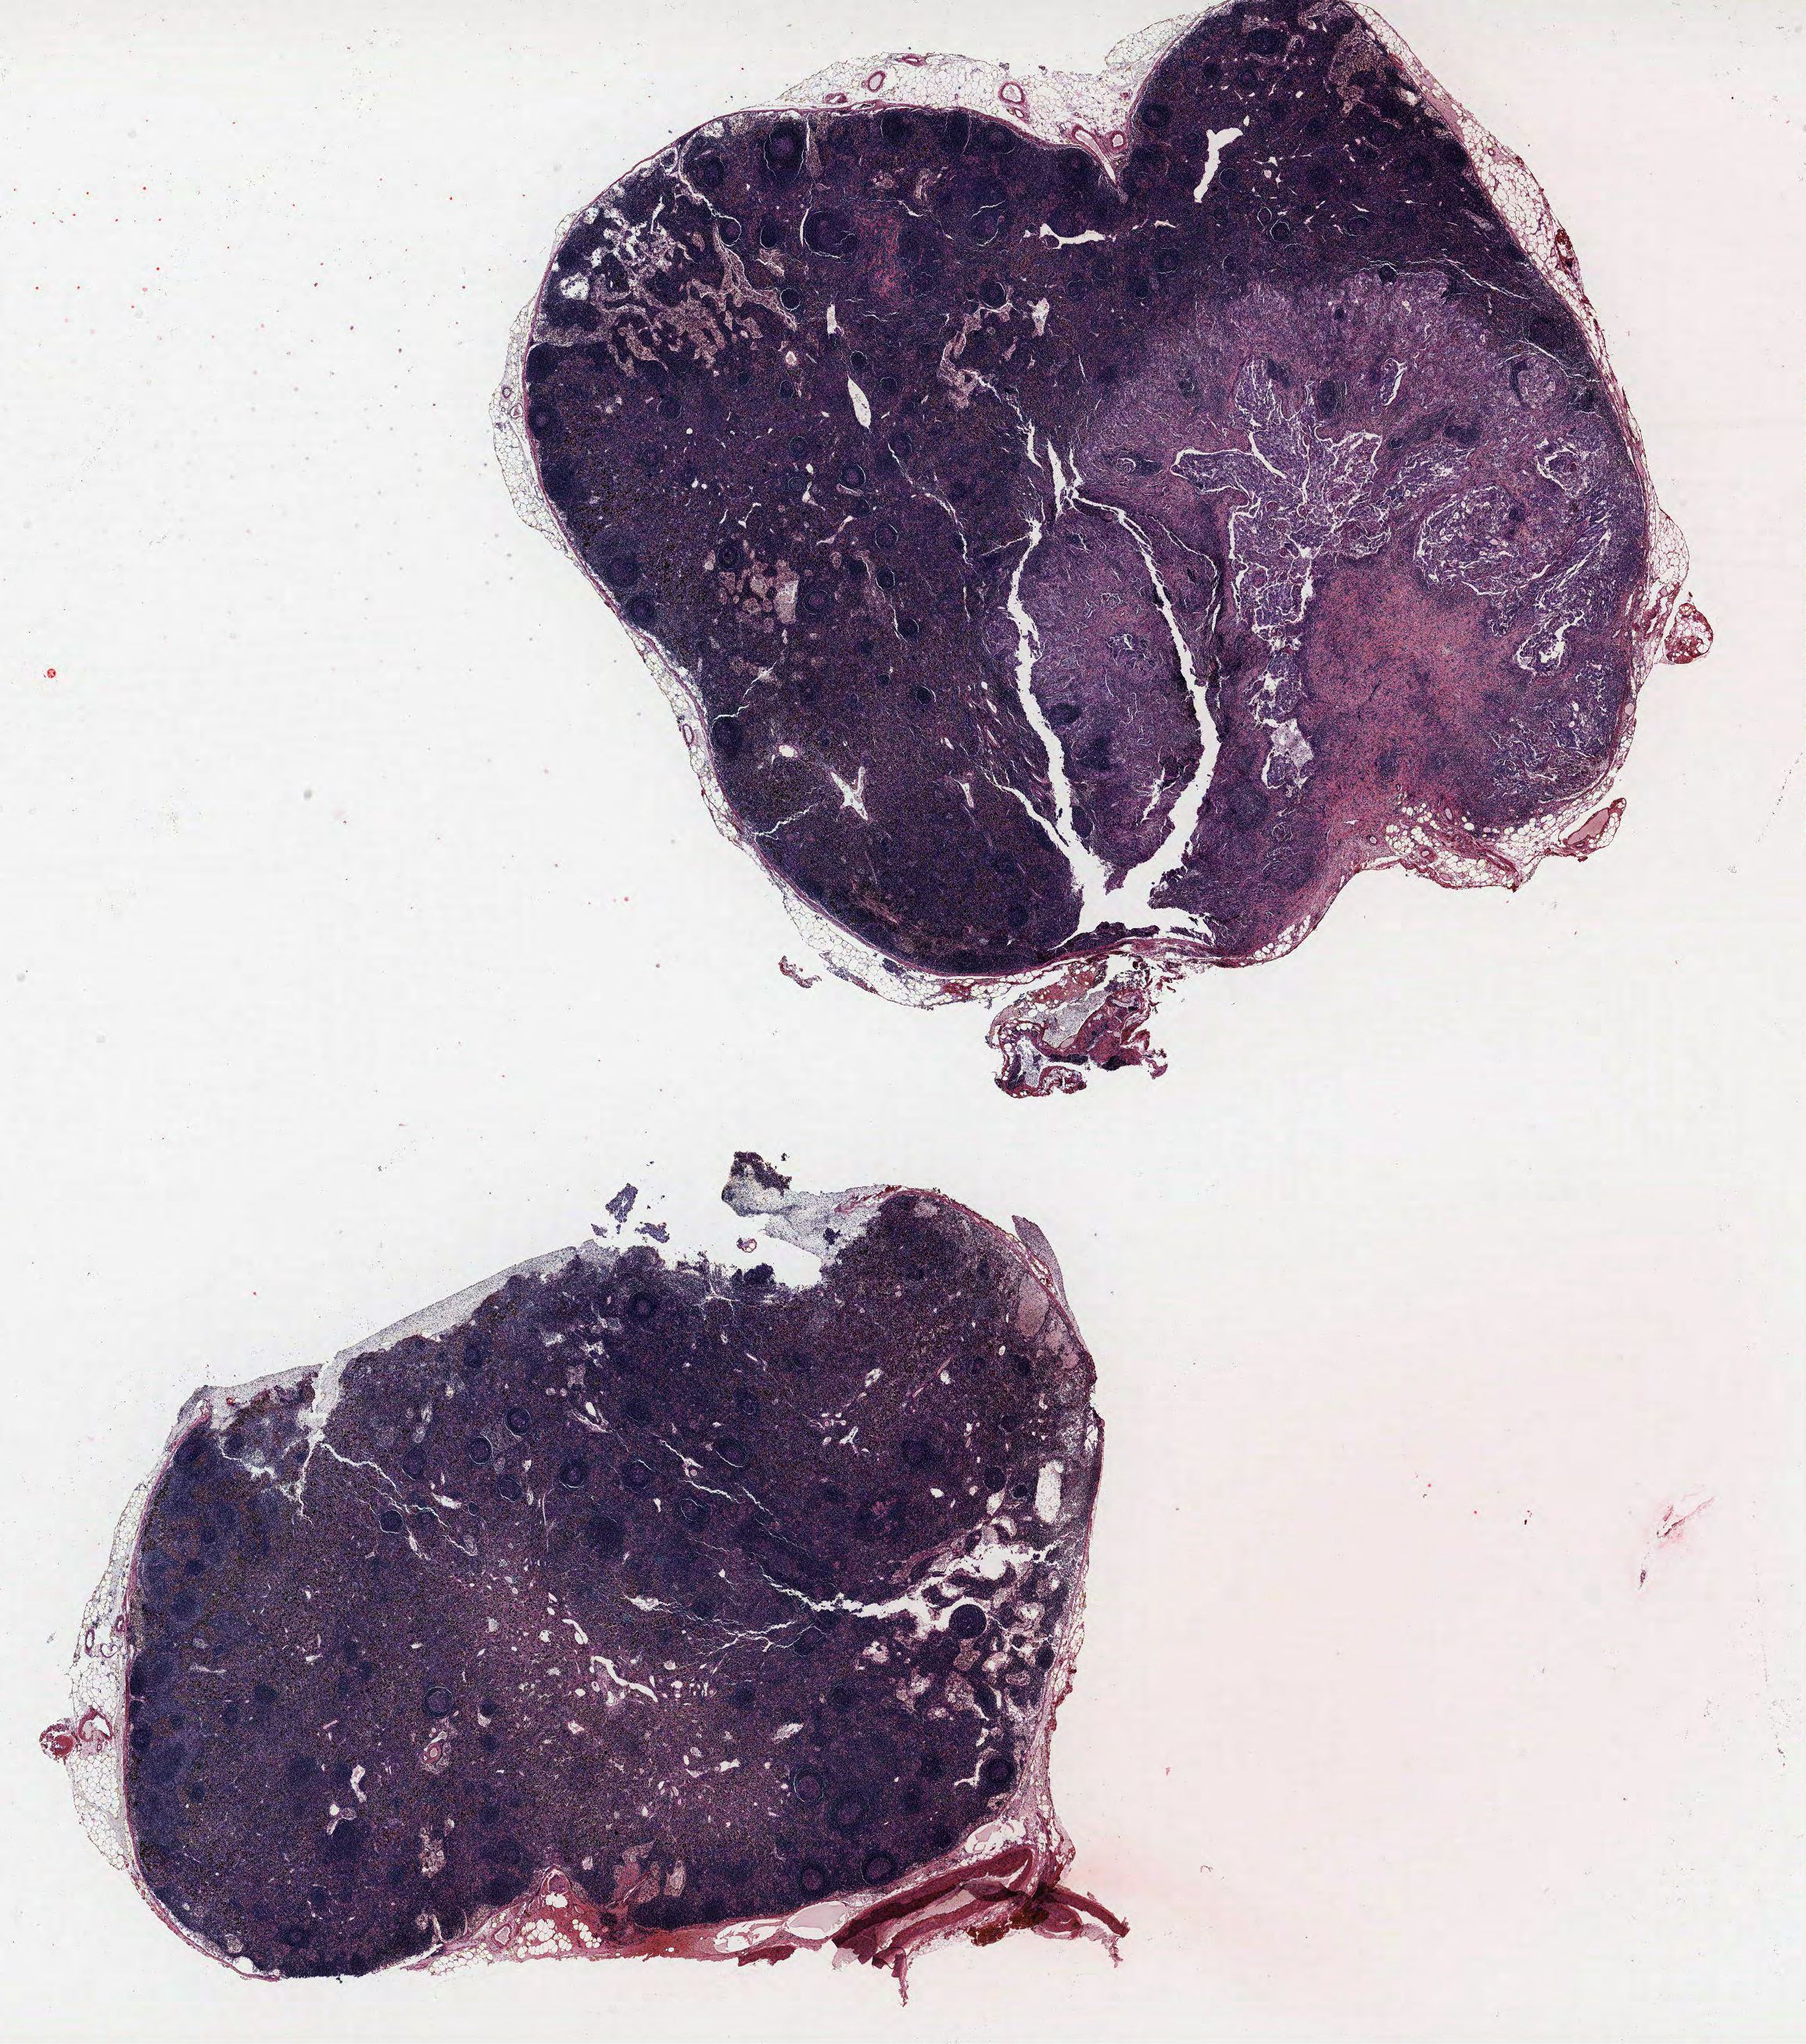
Whole-slide histology image, H&E — whole scanned area (about 18.5 x 20.9 mm) shown as a low-resolution overview, FFPE section, lung tissue. Male, age 56 at enrolment. Current smoker at enrolment. Grade: poorly differentiated (G3).
* participant's lung-cancer diagnosis: Adenocarcinoma, NOS
* stage (AJCC 6th edition): IIB
* tumour size (pathology): 60 mm
* ICD-O-3 topography: upper lobe of lung (C34.1)
* primary tumour location (clinical record): right upper lobe